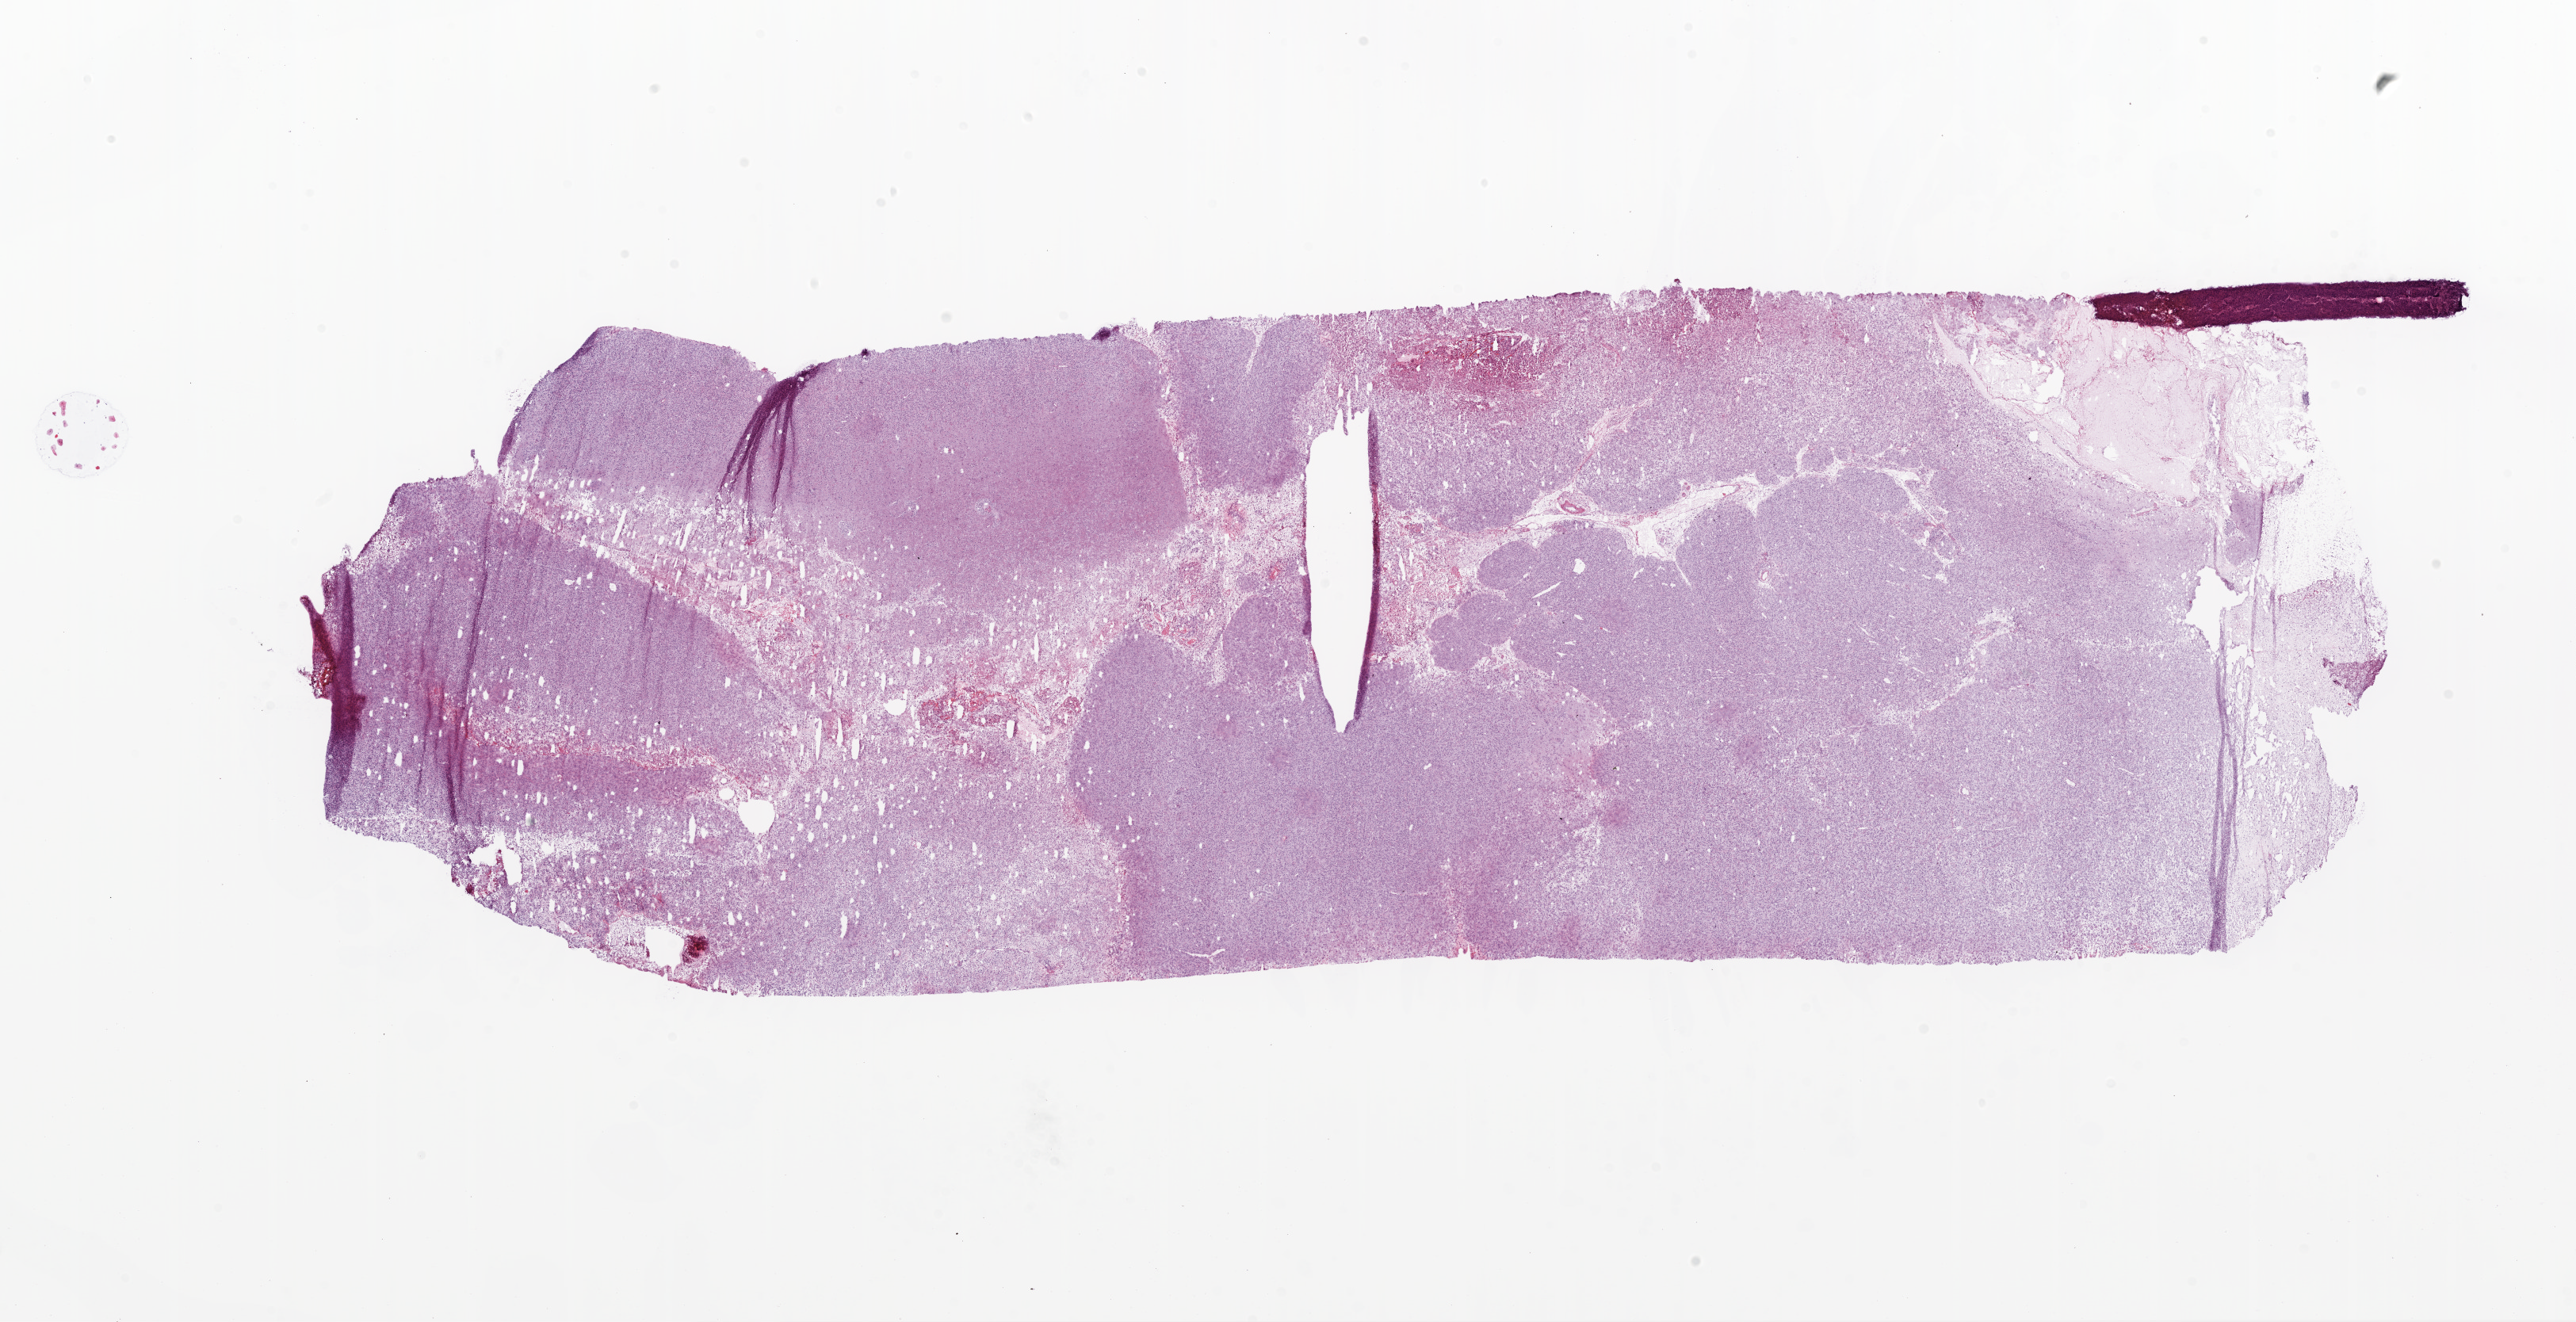
Digitized Hematoxylin and eosin (H&E) stained tissue section (whole slide), low-resolution overview of the scanned area, about 26.1 x 13.4 mm (acquisition: 20x scan), frozen section, primary tumour sample from the brain. Female, age 72 years at initial diagnosis. Slide review estimates, as recorded: tumour cells 95%, tumour nuclei 85%, normal cells 0%, stromal cells 0%, necrosis 5%.
Histologic diagnosis: Glioblastoma.